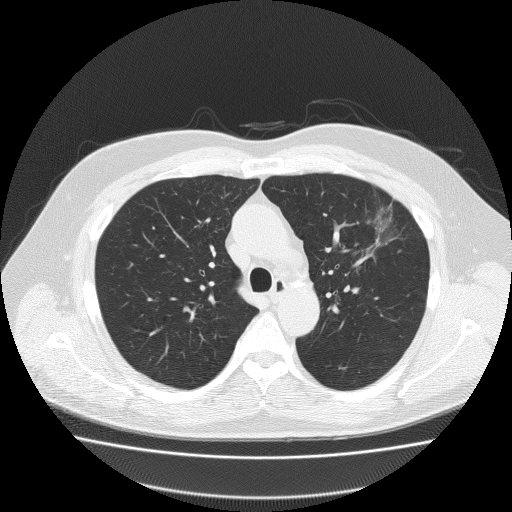
Low-dose screening chest CT, axial slice, baseline screening round, lung window (W 1500 / L -600 HU), 2 mm slice thickness, lung (sharp) reconstruction kernel (FC51). Male, age 62 years at enrolment. Former smoker at enrolment.
Expert reader's lesion annotation, bounding box <360,193,428,258> (left, top, right, bottom; pixels). Reader record for this screening exam (exam-level; its link to the box is not recorded): non-calcified nodule or mass ≥4 mm, left upper lobe, 18 × 8 mm, spiculated (stellate) margins, soft tissue attenuation. Participant outcome: lung cancer diagnosed 49 days after this screen — bronchiolo-alveolar adenocarcinoma, NOS, left upper lobe, well differentiated (G1), stage IA (AJCC 6th edition), 25 mm at pathology.